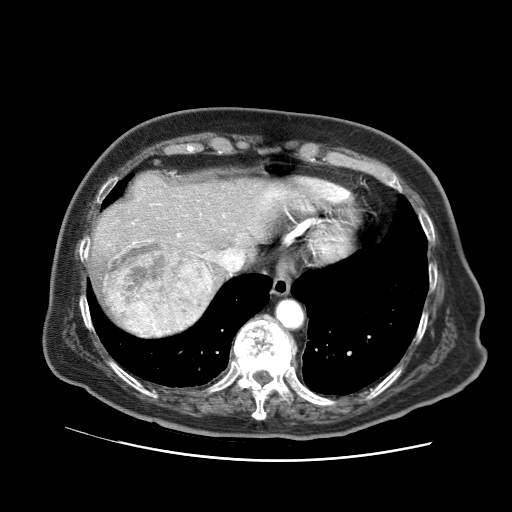
Contrast-enhanced abdominal CT (liver protocol), one axial slice. Slice 57 of 73 in the series (ordered by position). 120 kVp. Soft-tissue window (W 400 / L 40 HU). 2.5 mm slice thickness. 512 × 512 image matrix, field of view 380 × 380 mm. Case-level facts recorded for this patient, not image findings: diagnosis: hepatocellular carcinoma (patient treated with transarterial chemoembolisation; whether this scan precedes or follows treatment is not stated here); TNM stage (as recorded): Stage-I; Child-Pugh class: A; tumour differentiation: well differentiated.
Outlined on this slice (semi-automatic segmentation, software-assisted and operator-edited):
- liver parenchyma outside the tumour (the mass and vessels are separate outlines, so this box may not span the whole liver): bounding box (x1, y1, x2, y2) in pixels: (87, 172, 288, 338)
- mass: (104, 244, 214, 335)
- liver vessels: (133, 192, 280, 320)